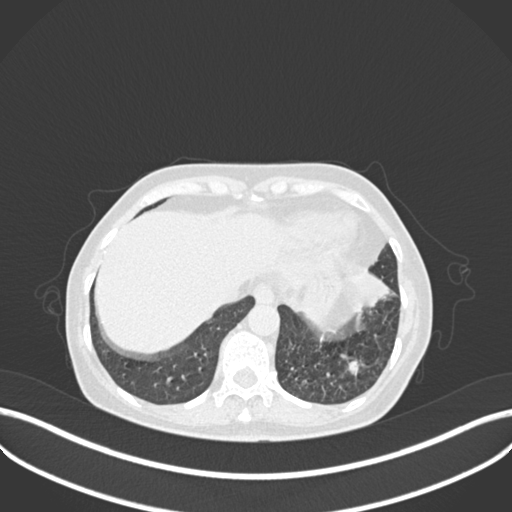
Chest CT, one axial slice. Position 48 of 270 along the scan axis. Reconstruction kernel B30f. 120 kVp. Lung window (W 1500 / L -600 HU). 1 mm slice thickness. 512 × 512 image matrix, field of view 400 × 400 mm. Patient: female, 63 years. Case-level facts recorded for this patient, not image findings: clinical TNM (as recorded): T1b N0 M0; histopathological grade: G2-3.
Structures marked on this image (bounding box drawn by a radiologist):
- lung tumour (recorded histology: adenocarcinoma): bounding box (x1, y1, x2, y2) in pixels: (340, 265, 401, 315)